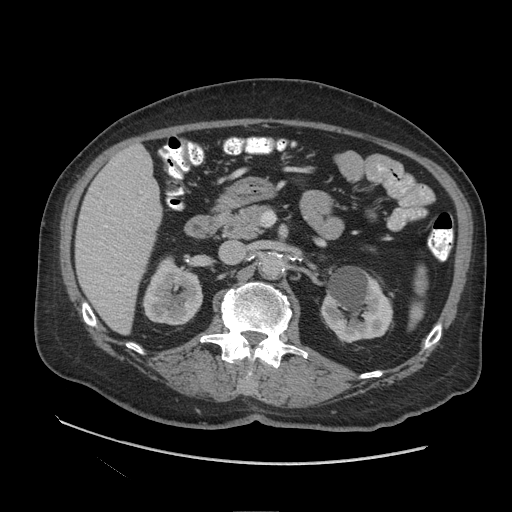
Contrast-enhanced abdominal CT (liver protocol), one axial slice. Slice 42 of 109 in the series (ordered by position). Reconstruction kernel STANDARD. Soft-tissue window (W 400 / L 40 HU). 2.5 mm slice thickness. 512 × 512 image matrix, field of view 420 × 420 mm. Case-level facts recorded for this patient, not image findings: diagnosis: hepatocellular carcinoma (patient treated with transarterial chemoembolisation; whether this scan precedes or follows treatment is not stated here); TNM stage (as recorded): Stage-I; Child-Pugh class: A.
Outlined on this slice (semi-automatically segmented with operator editing):
- liver parenchyma outside the tumour (the mass and vessels are separate outlines, so this box may not span the whole liver): bounding box [x1, y1, x2, y2] px = [76, 144, 162, 334]
- liver vessels: [99, 191, 142, 290]